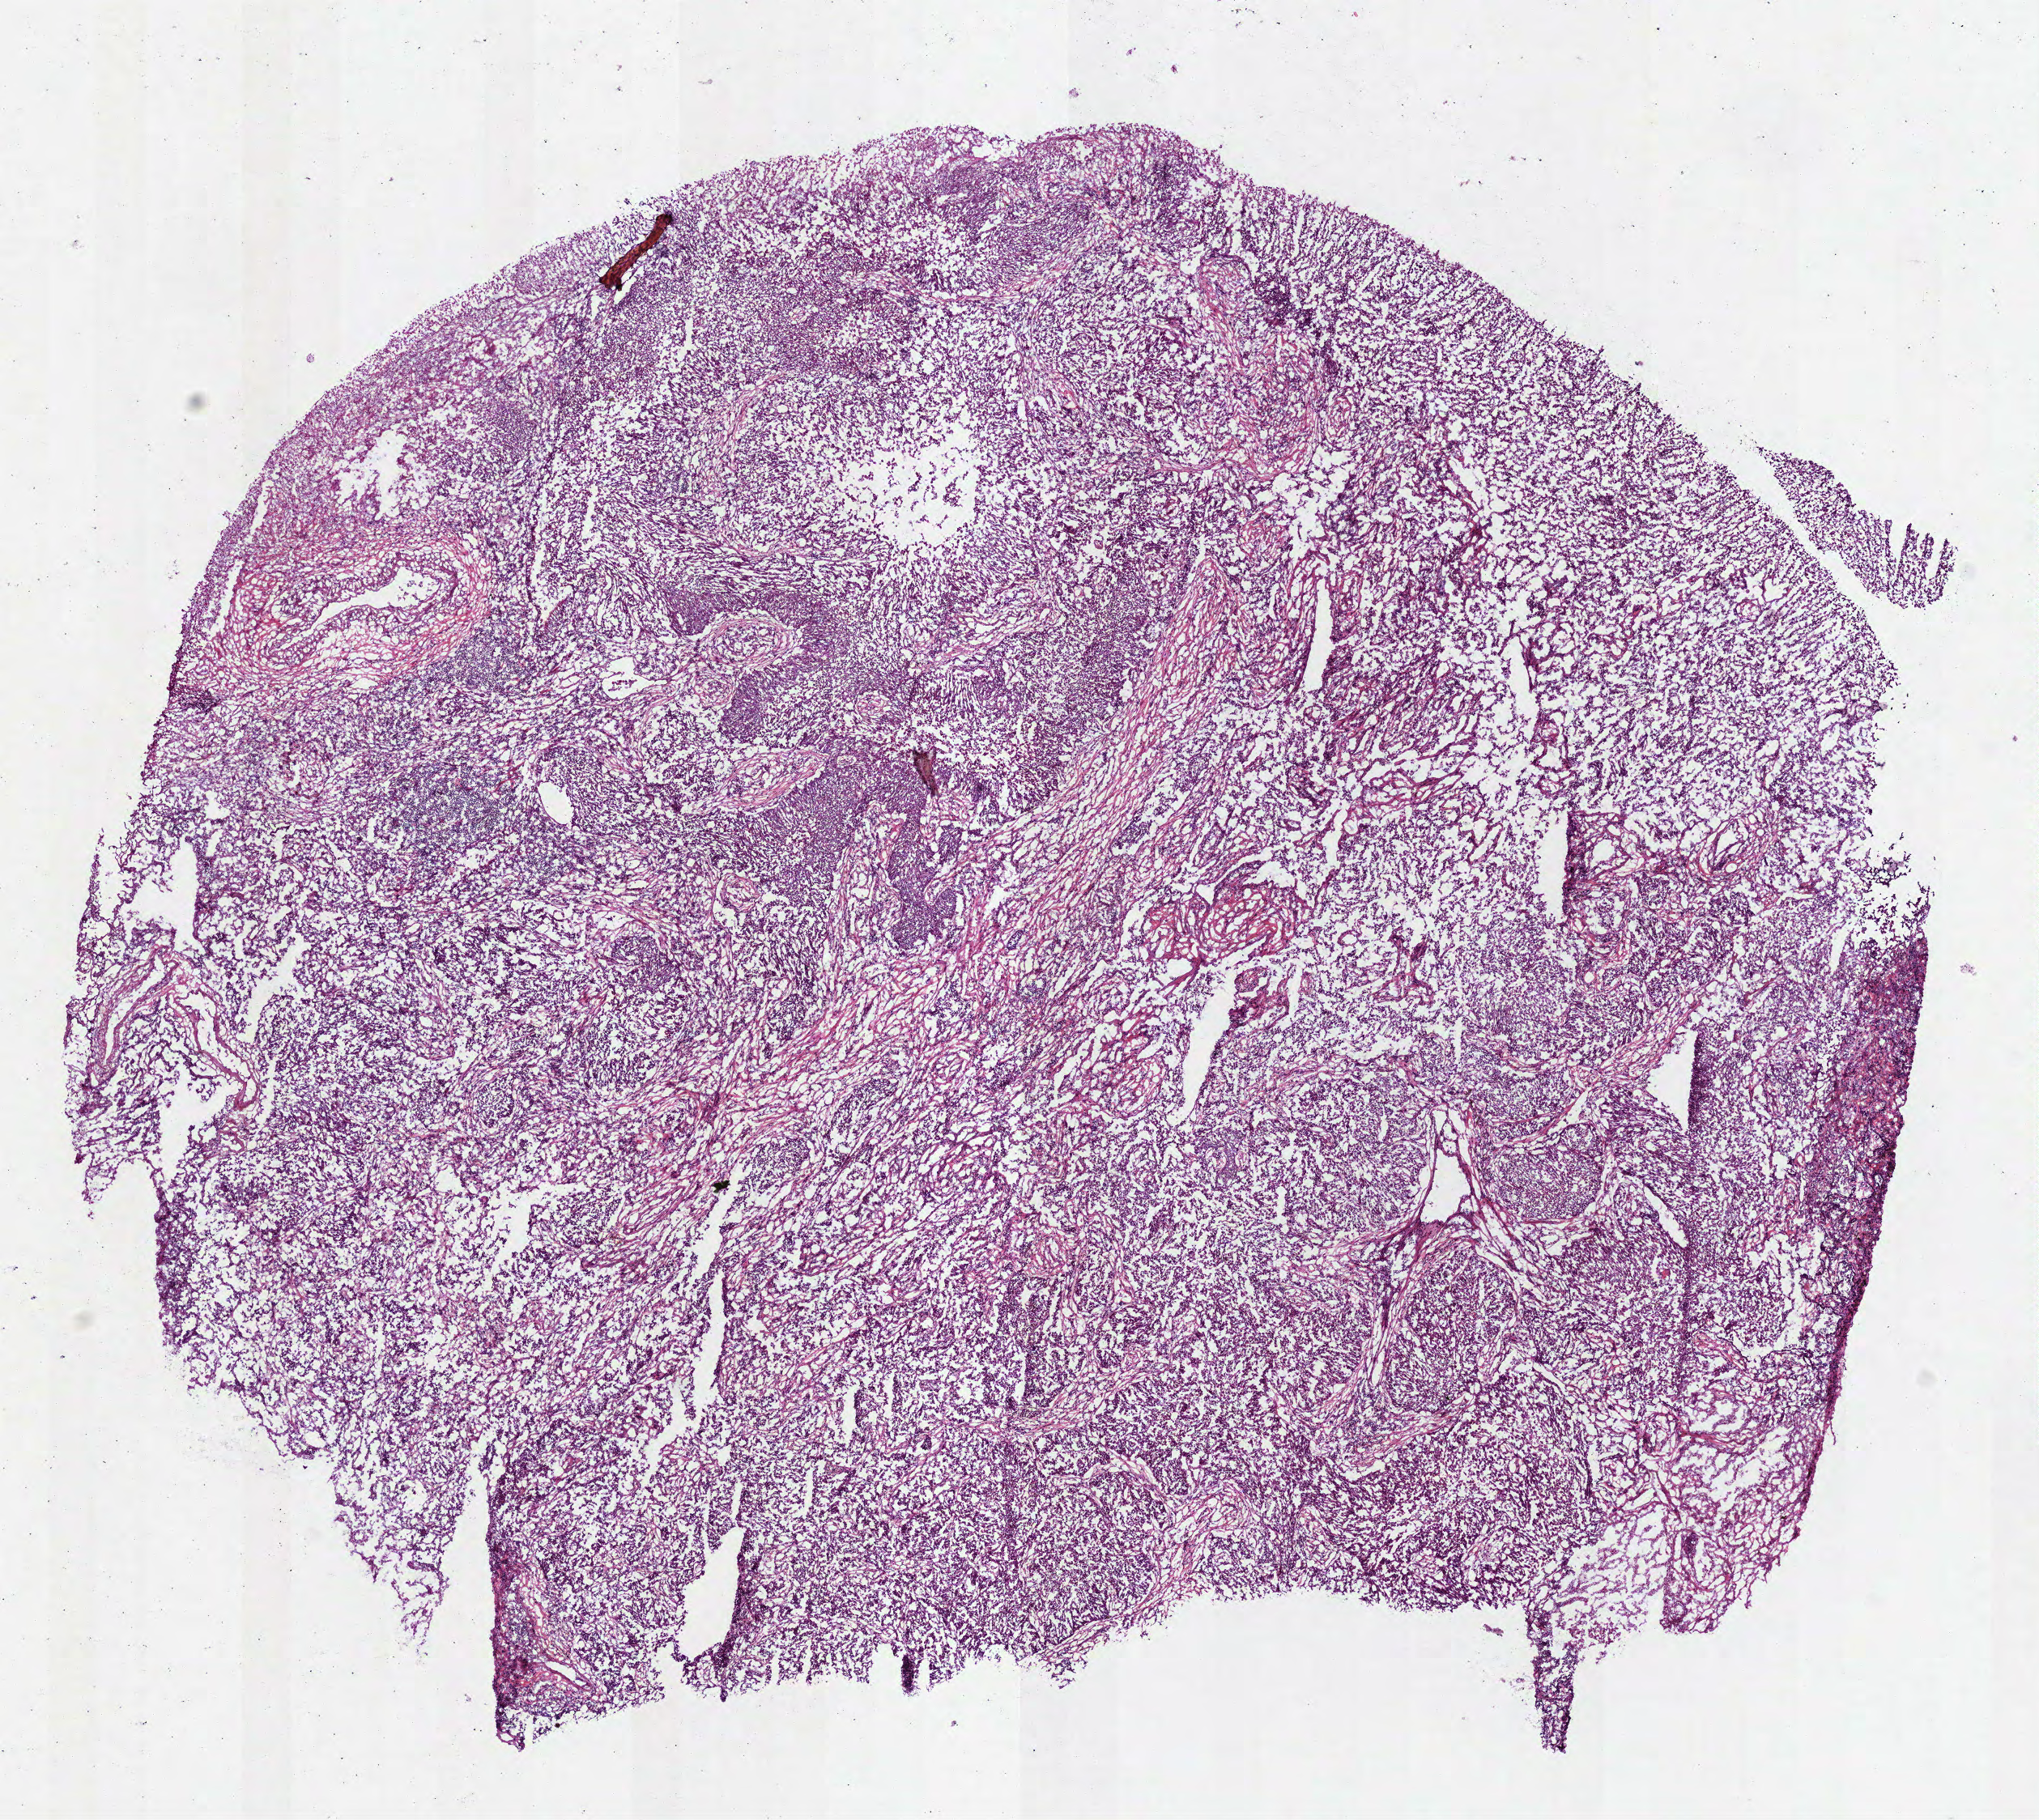
Whole-slide histology image, Hematoxylin and eosin (H&E) stained — a low-resolution overview of the entire scanned area, about 10.2 x 9.1 mm (acquisition: 40x scan). Frozen section. Sample: primary tumour, lung. Female patient; age at initial diagnosis 62 years. Slide review estimates, as recorded: tumour cells 89%, tumour nuclei 70%.
Diagnosis: Squamous cell carcinoma, NOS (lower lobe, lung).